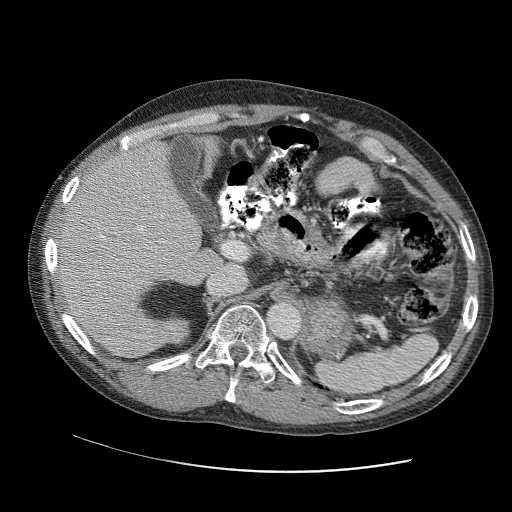
Contrast-enhanced abdominal CT (liver protocol), one axial slice. Position 66 of 109 along the scan axis. Soft-tissue window (W 400 / L 40 HU). 2.5 mm slice thickness. 512 × 512 image matrix, field of view 400 × 400 mm. From the clinical record (not read from this slice): diagnosis: hepatocellular carcinoma (patient treated with transarterial chemoembolisation; whether this scan precedes or follows treatment is not stated here); TNM stage (as recorded): Stage-IIIC; Child-Pugh class: B; tumour differentiation: well differentiated; tumour nodularity: uninodular.
Structures marked on this image (semi-automatically segmented with operator editing):
- liver parenchyma outside the tumour (the mass and vessels are separate outlines, so this box may not span the whole liver): box from (x=54, y=140) to (x=200, y=358) px
- mass: (x=170, y=321)–(x=187, y=343)
- liver vessels: (x=63, y=159)–(x=165, y=323)